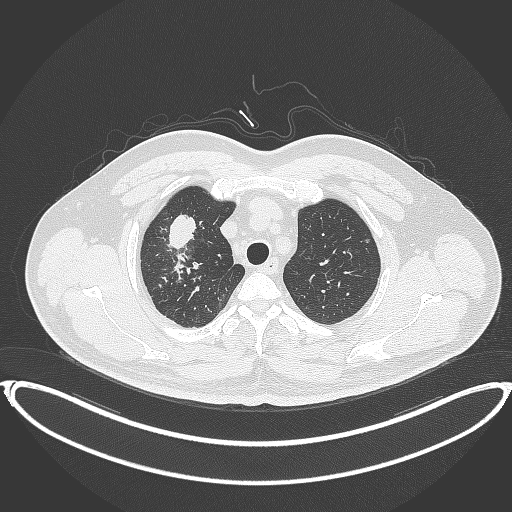
Chest CT, one axial slice. Position 317 of 399 along the scan axis. 120 kVp. Lung window (W 1500 / L -600 HU). 512 × 512 image matrix, field of view 445 × 445 mm. Male patient, age 53 years. Case-level facts recorded for this patient, not image findings: clinical TNM (as recorded): T2a N0 M0.
Structures marked on this image (rectangle marked by the reading radiologist):
- lung tumour (recorded histology: adenocarcinoma): bounding box <167,214,201,251> (left, top, right, bottom; pixels)